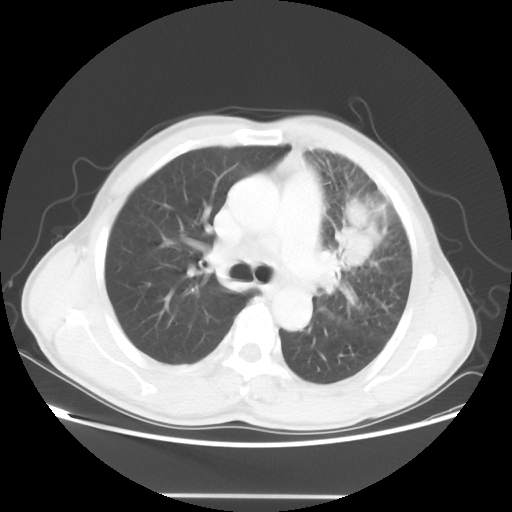
Chest CT, one axial slice; slice 34 of 55 in the series (ordered by position); reconstruction kernel STANDARD; 100 kVp; lung window (W 1500 / L -600 HU); 5 mm slice thickness; 512 × 512 image matrix. Male patient, age 60 years. From the clinical record (not read from this slice): clinical TNM (as recorded): T3 N3 M0.
Structures marked on this image (rectangle marked by the reading radiologist):
- lung tumour (recorded histology: adenocarcinoma): bounding box [x1, y1, x2, y2] px = [334, 197, 381, 265]